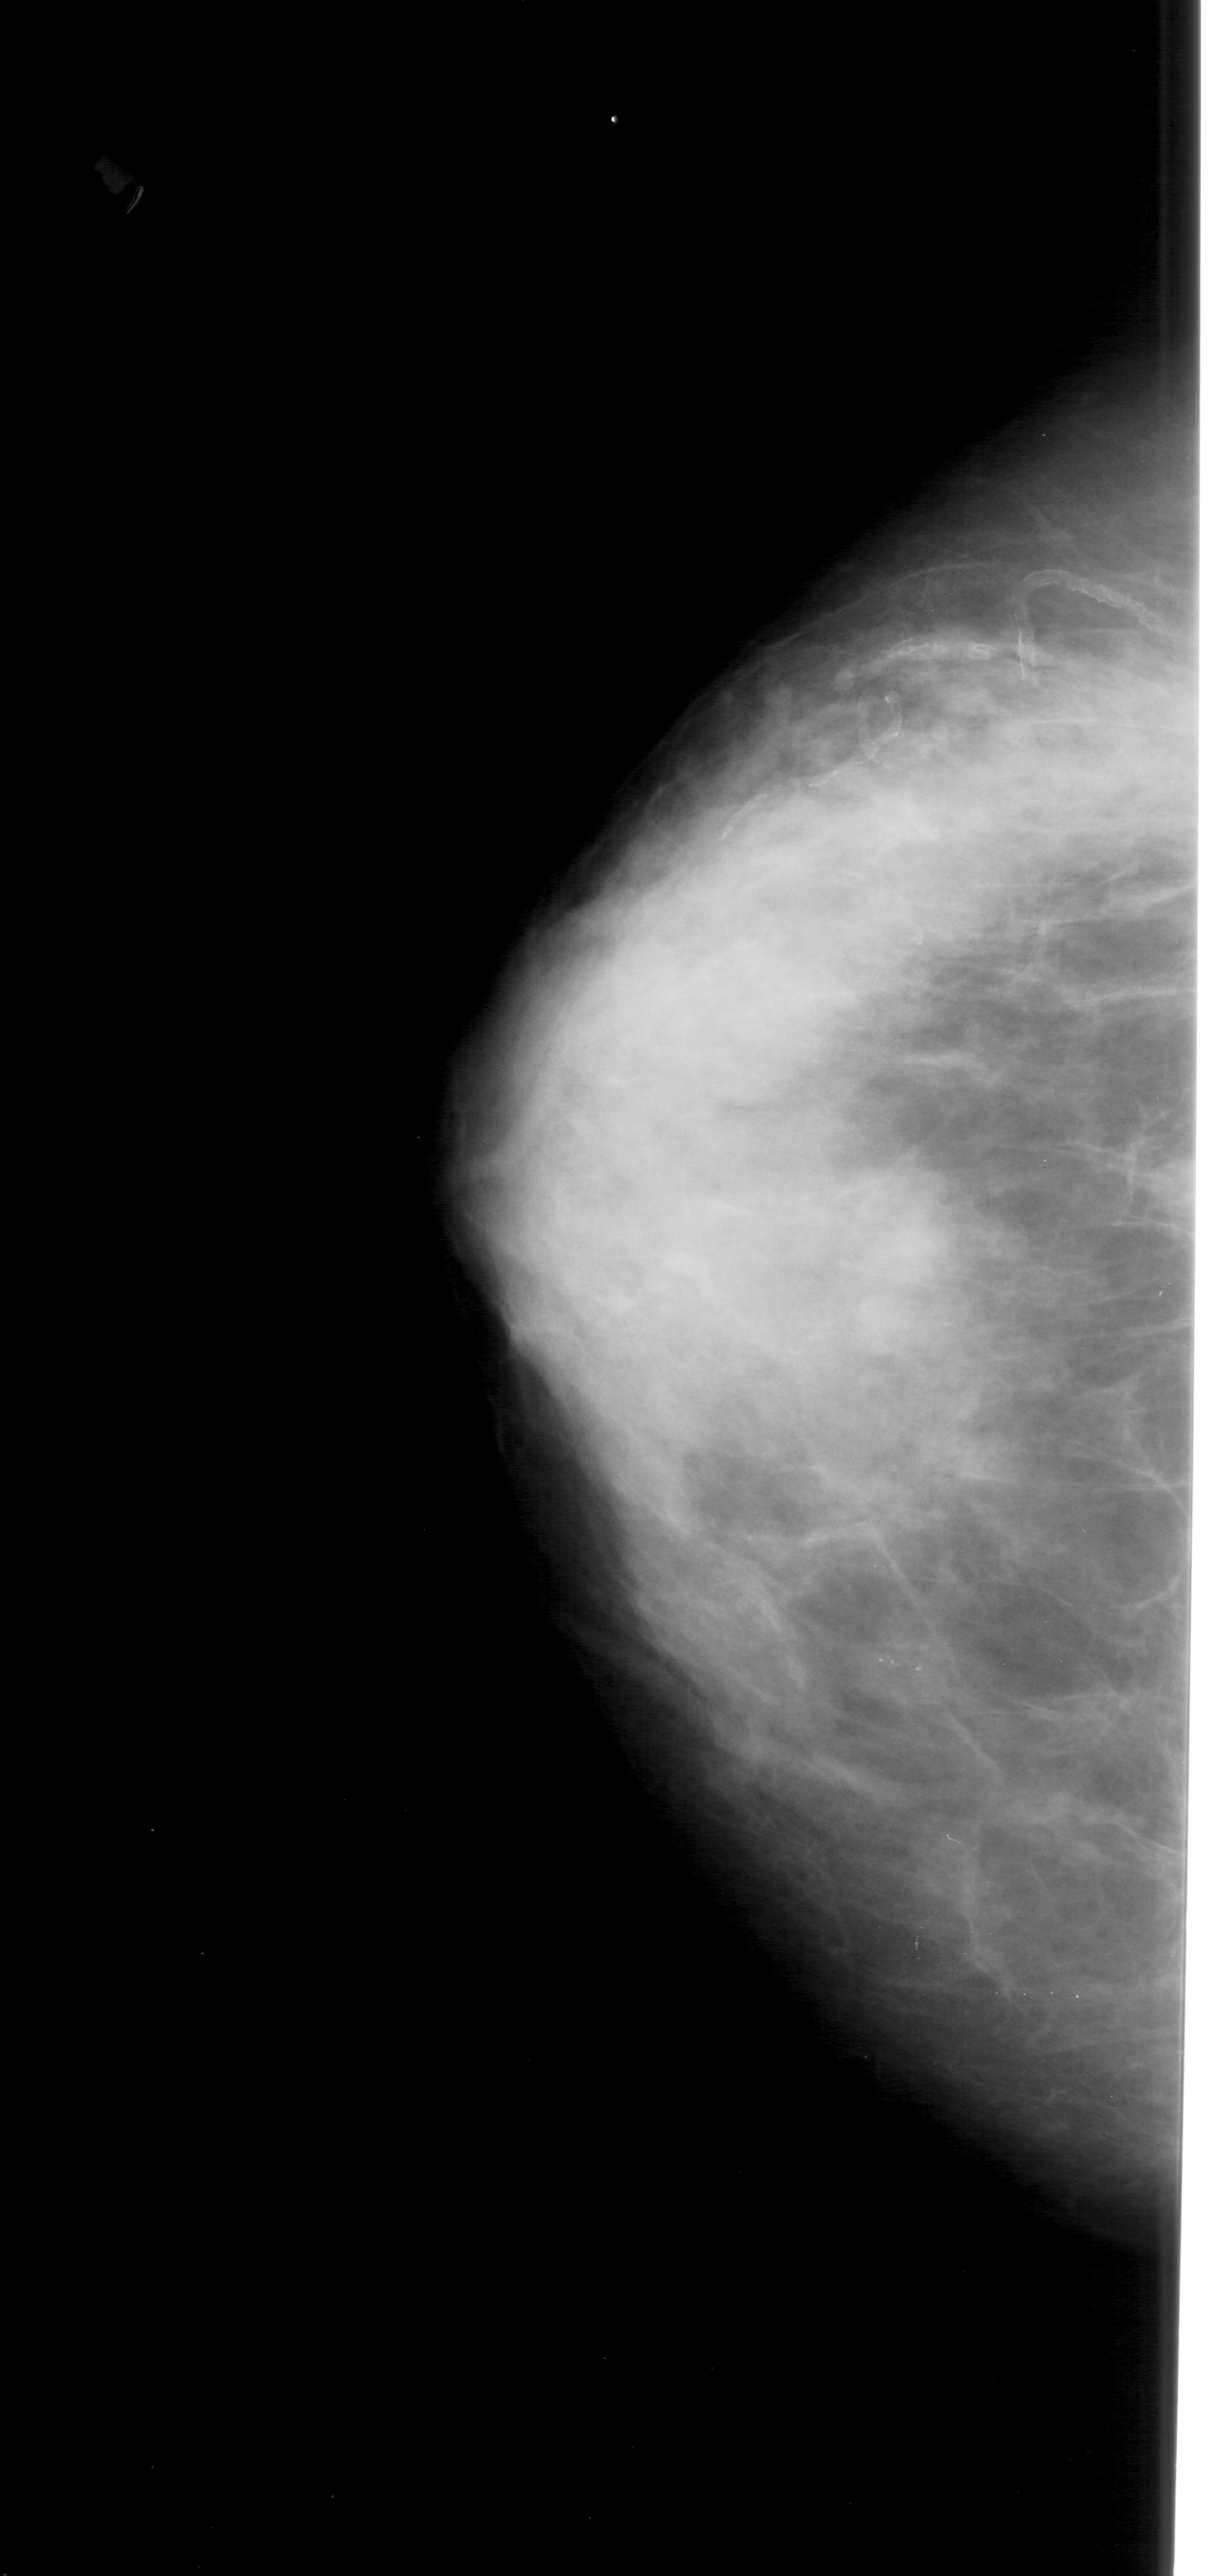
Digitized screen-film mammogram; left breast; craniocaudal (CC) view; breast composition: extremely dense (BI-RADS density category 4 of 4); 1209 × 2576 image matrix.
Marked abnormalities (boxes around the expert regions of interest):
- calcifications, morphology pleomorphic, distribution clustered; BI-RADS assessment category 4; pathology (as recorded): benign: bounding box <853,1635,968,1707> (left, top, right, bottom; pixels)